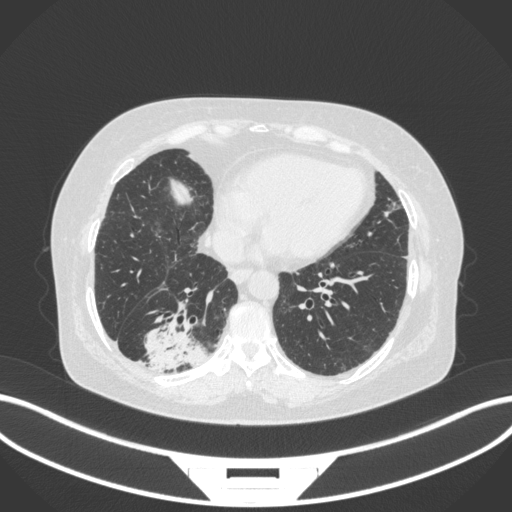
Chest CT, one axial slice. Slice 72 of 303 in the series (ordered by position). Lung window (W 1500 / L -600 HU). 1 mm slice thickness. 512 × 512 image matrix. Patient: female, 65 years. From the clinical record (not read from this slice): clinical TNM (as recorded): T2b N1 M0.
Structures marked on this image (rectangle marked by the reading radiologist):
- lung tumour (recorded histology: adenocarcinoma): bounding box [x1, y1, x2, y2] px = [138, 324, 215, 373]